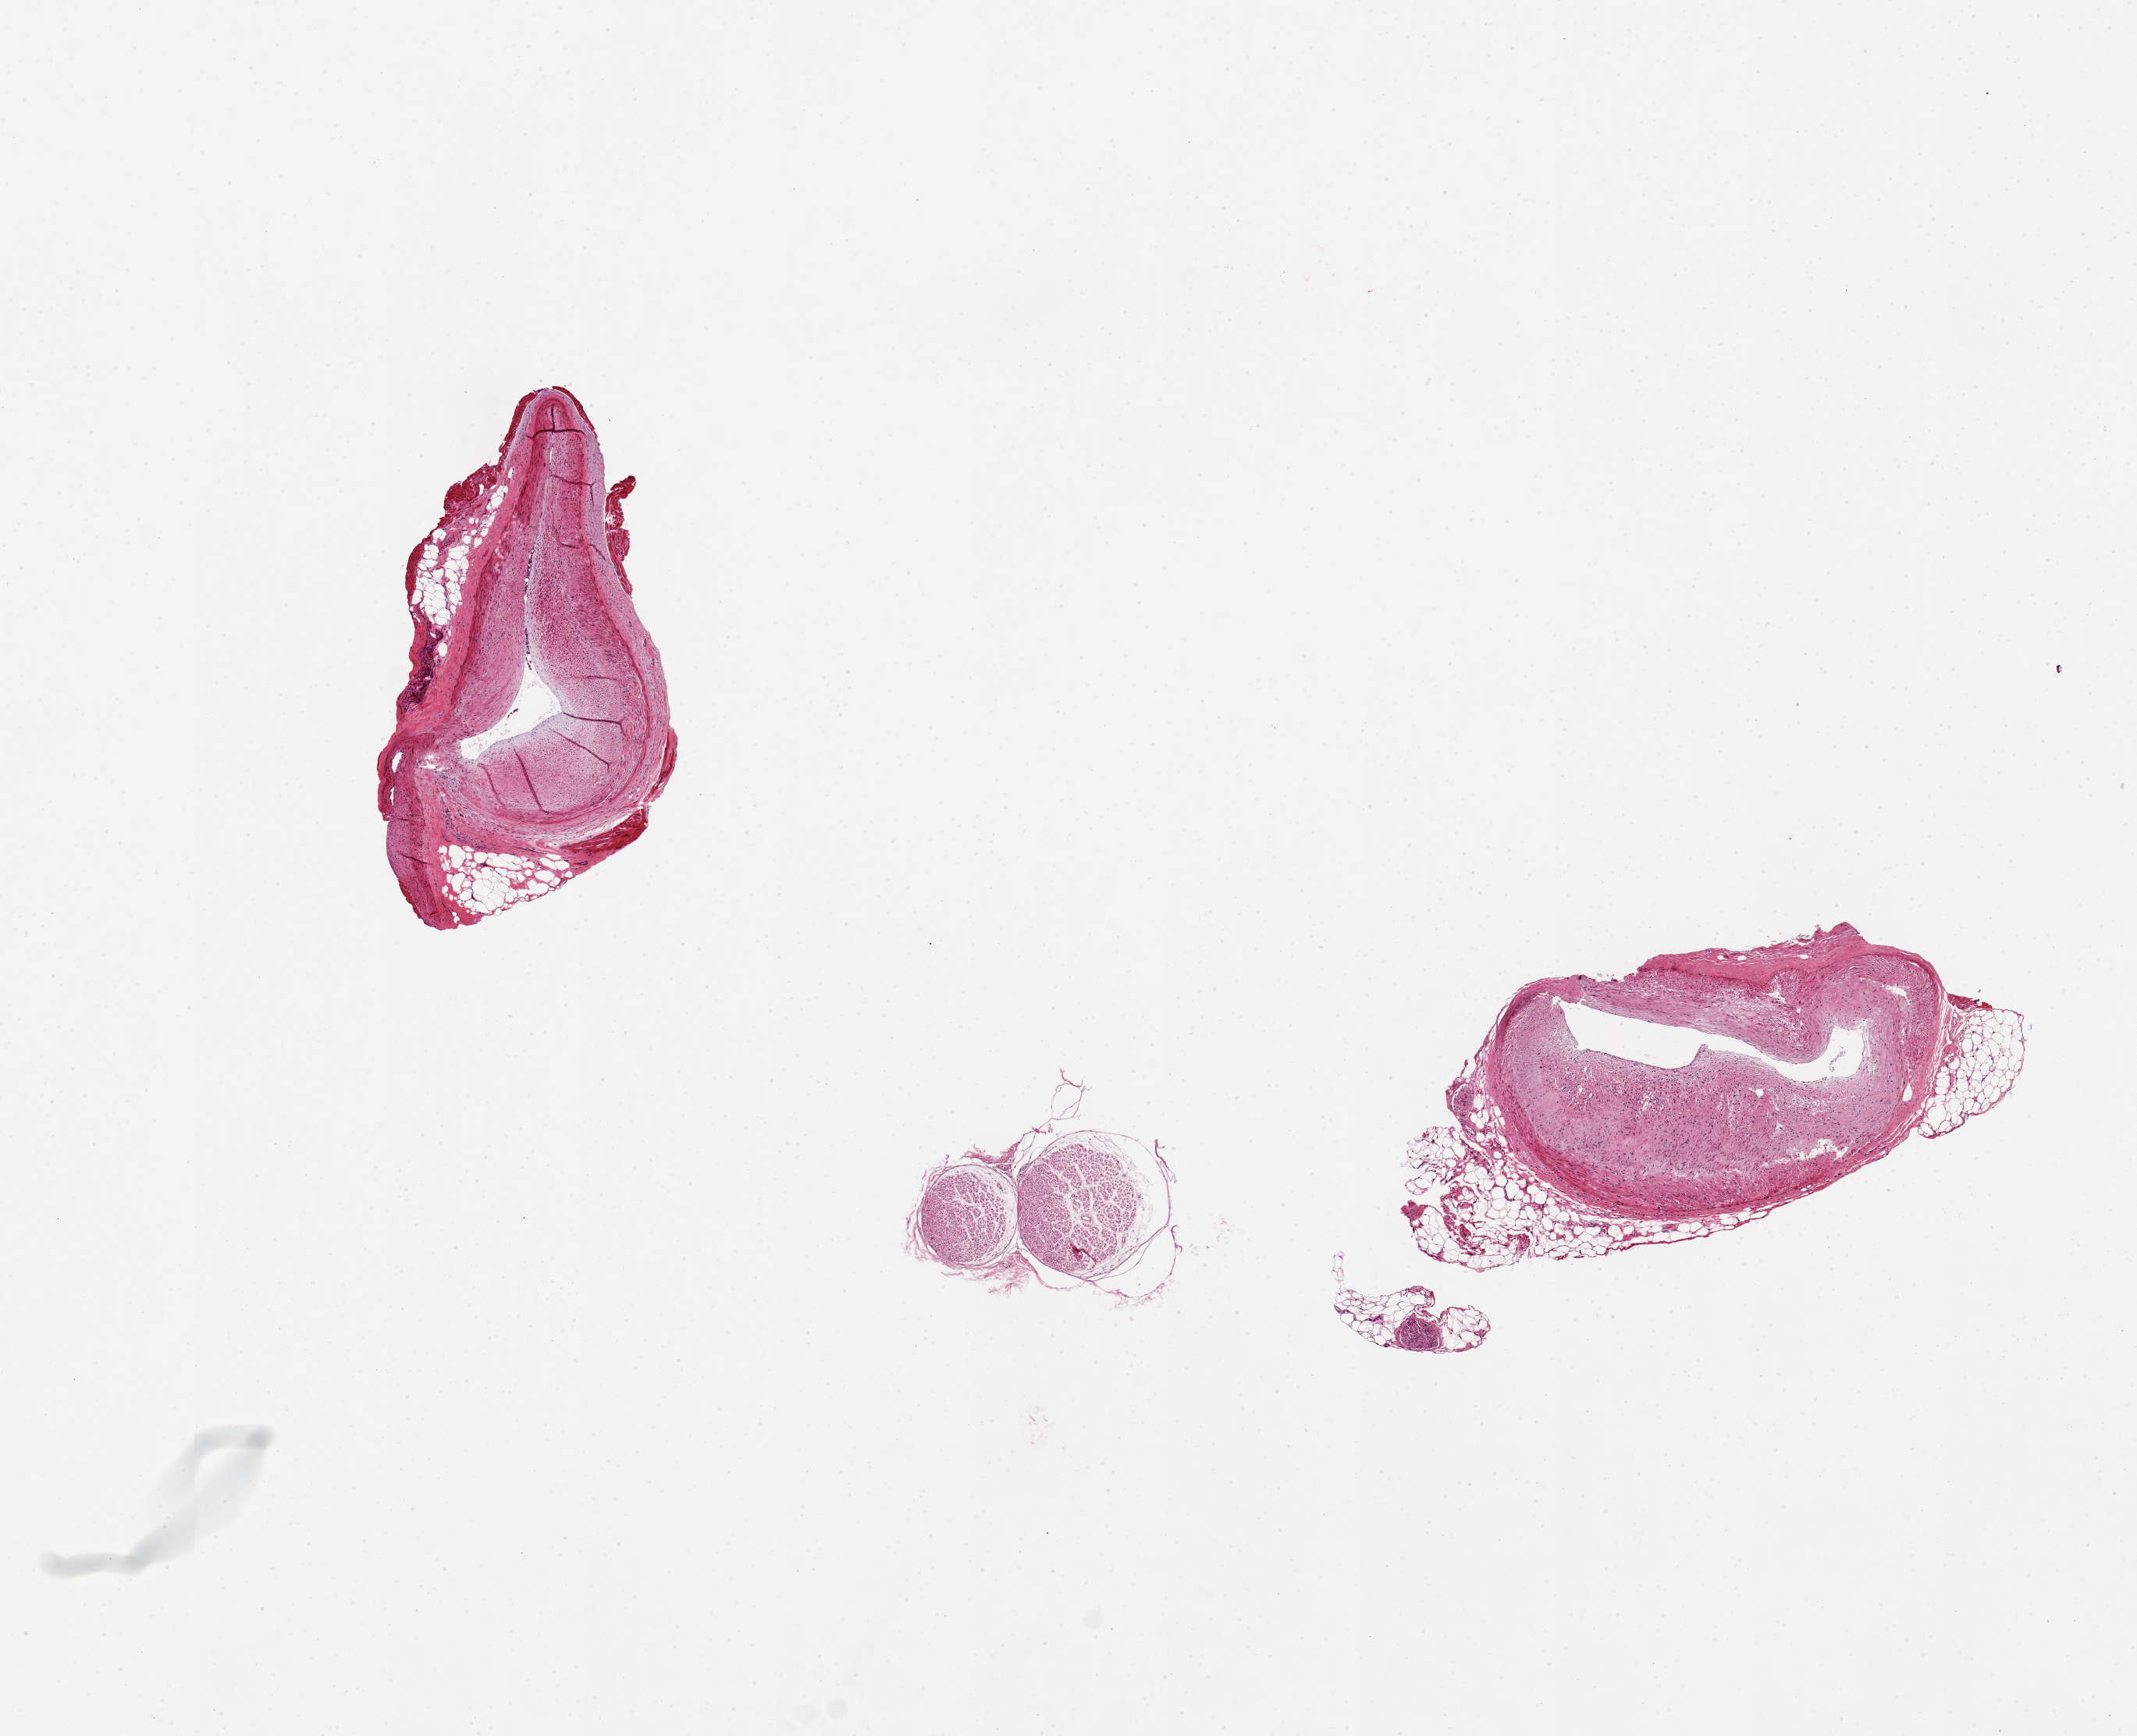
Whole-slide image, hematoxylin and eosin (H&E) stain, a low-resolution overview of the entire scanned area, about 10.8 x 8.8 mm (slide scanned at 20x). PAXgene-fixed, paraffin-embedded tissue. Section of coronary artery (target tissue). Tissue donor sample. Donor sex: male.
* reviewer comment on this tissue sample: 3 pieces, two of artery with narrowing of the lumen due to atheroma, both have small amount of attached adipose tissue. Small fragments of nerve also present